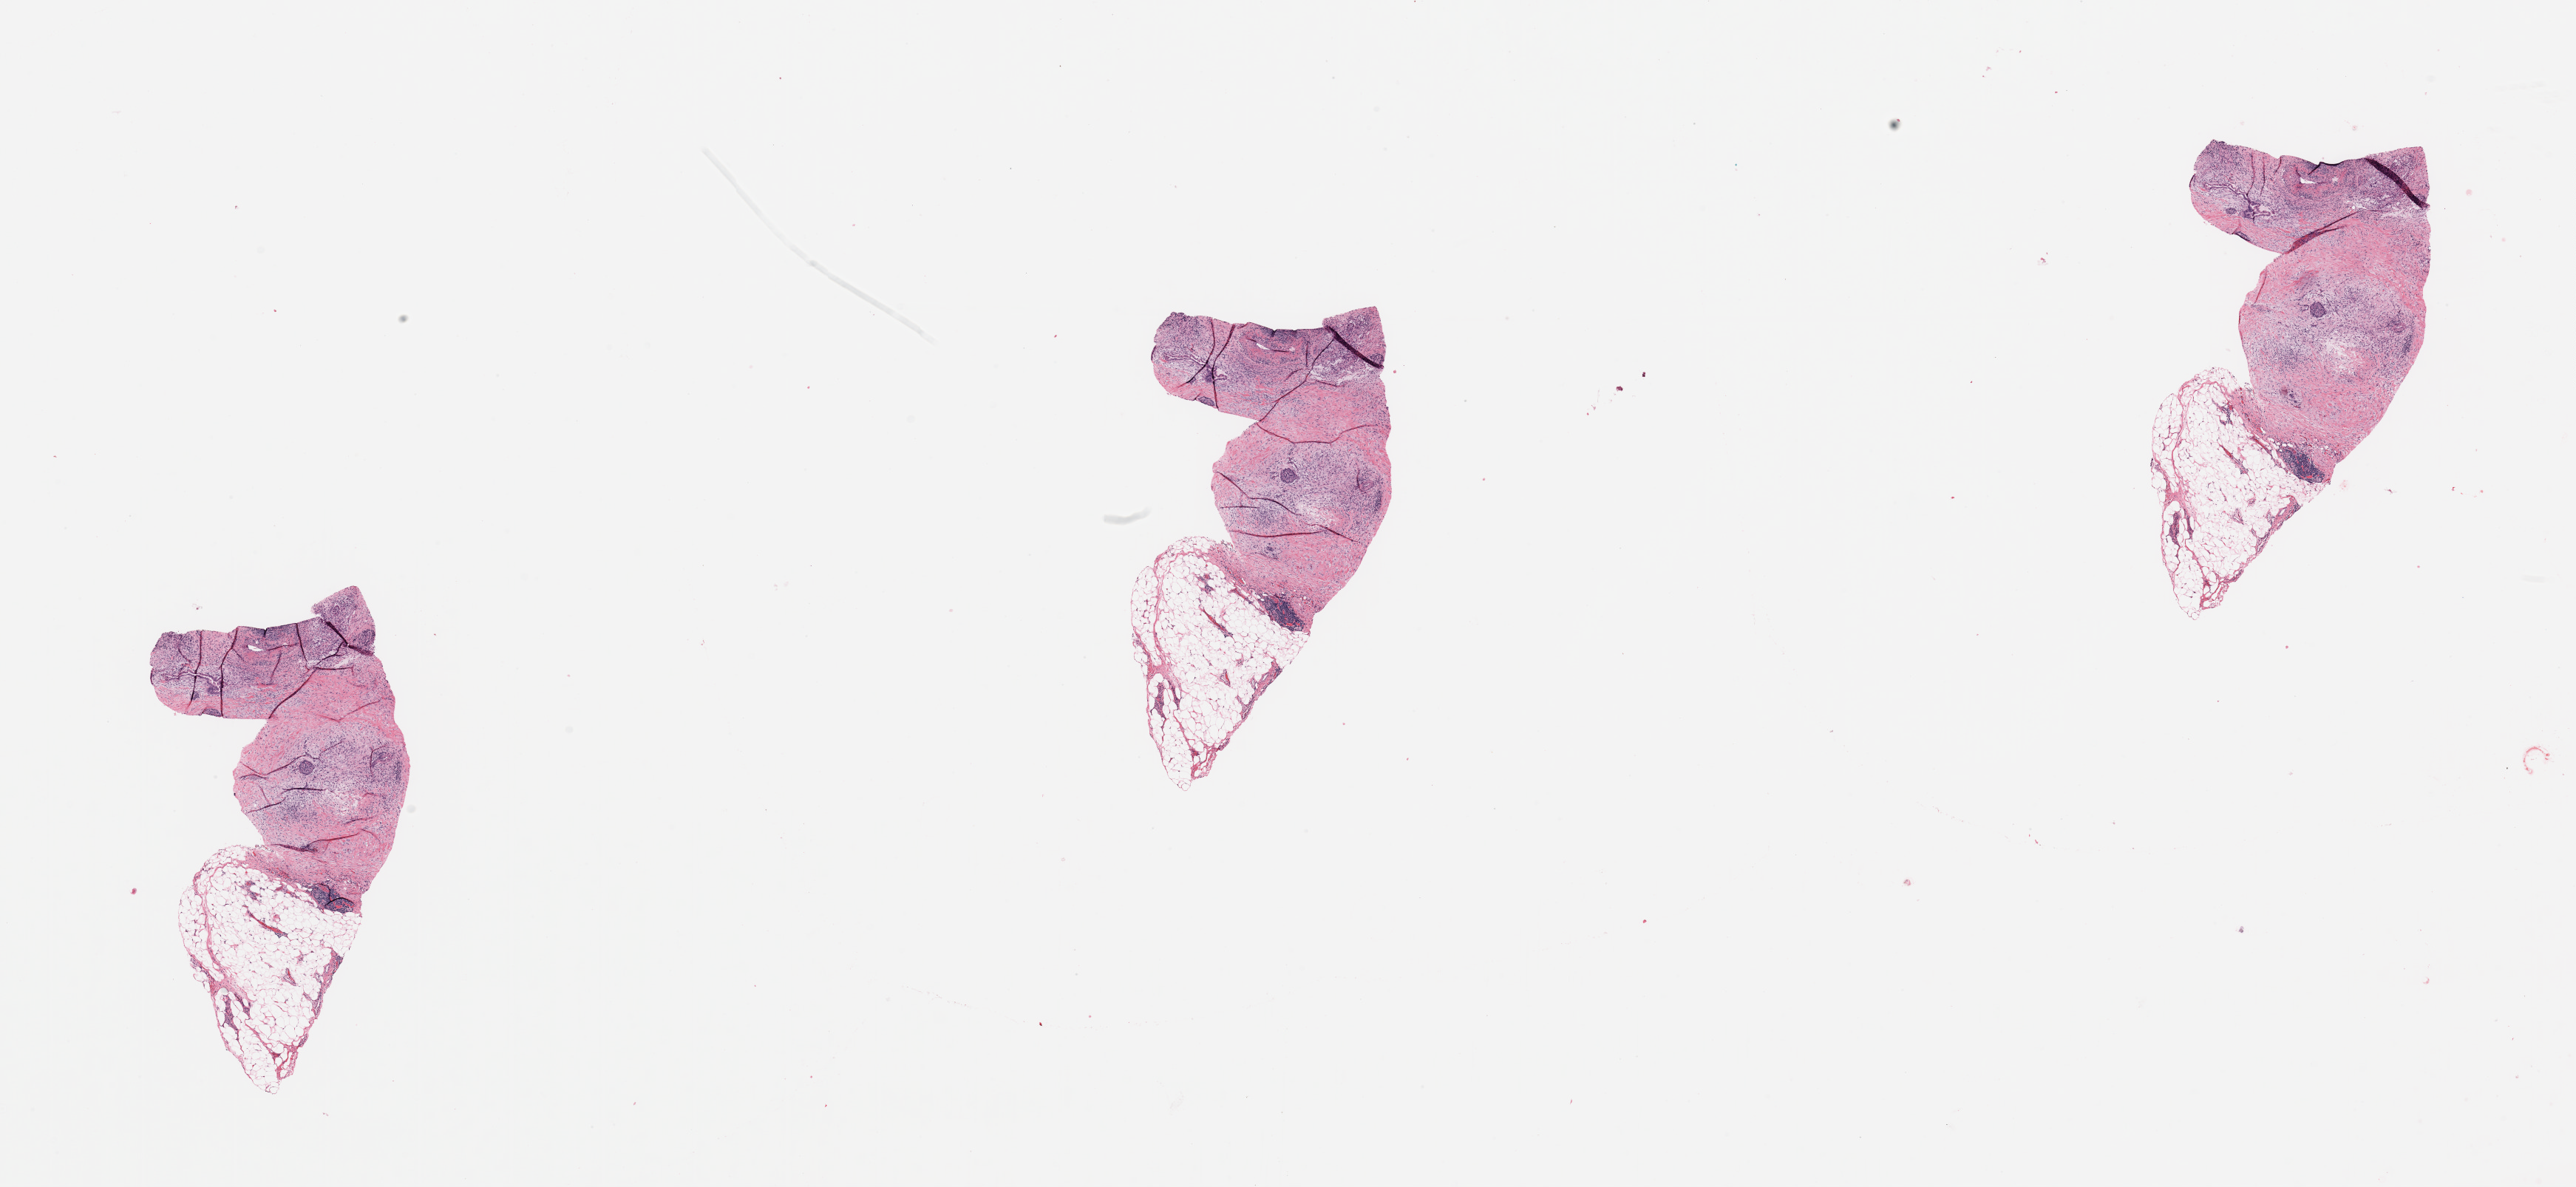
H&E-stained whole-slide image — shown as a low-resolution overview of the whole scanned area (about 27.6 x 12.7 mm, acquisition: 20x scan). Tumour tissue sample, pancreas. 75-year-old male patient.
Patient diagnosis (cohort enrolment): ductal adenocarcinoma (pancreas).